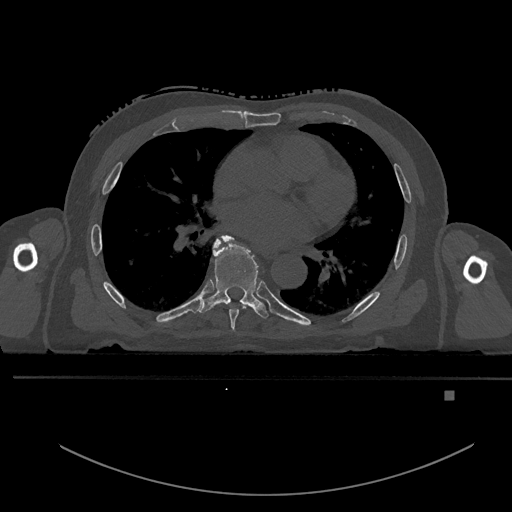
CT including the spine, one axial slice. Position 273 of 969 along the scan axis. Bone window (W 1800 / L 400 HU). 0.5 mm slice thickness. 512 × 512 image matrix, field of view 456 × 456 mm. Patient: male, 82 years. From the clinical record (not read from this slice): primary cancer: prostate; vertebrae with lytic lesions (as recorded): T11, T9, T8, T2.
Annotated regions visible in this slice (semi-automatic segmentation, software-assisted and operator-edited):
- T6 vertebra: bounding box [x1, y1, x2, y2] px = [215, 239, 248, 331]
- T7 vertebra: [199, 235, 269, 319]